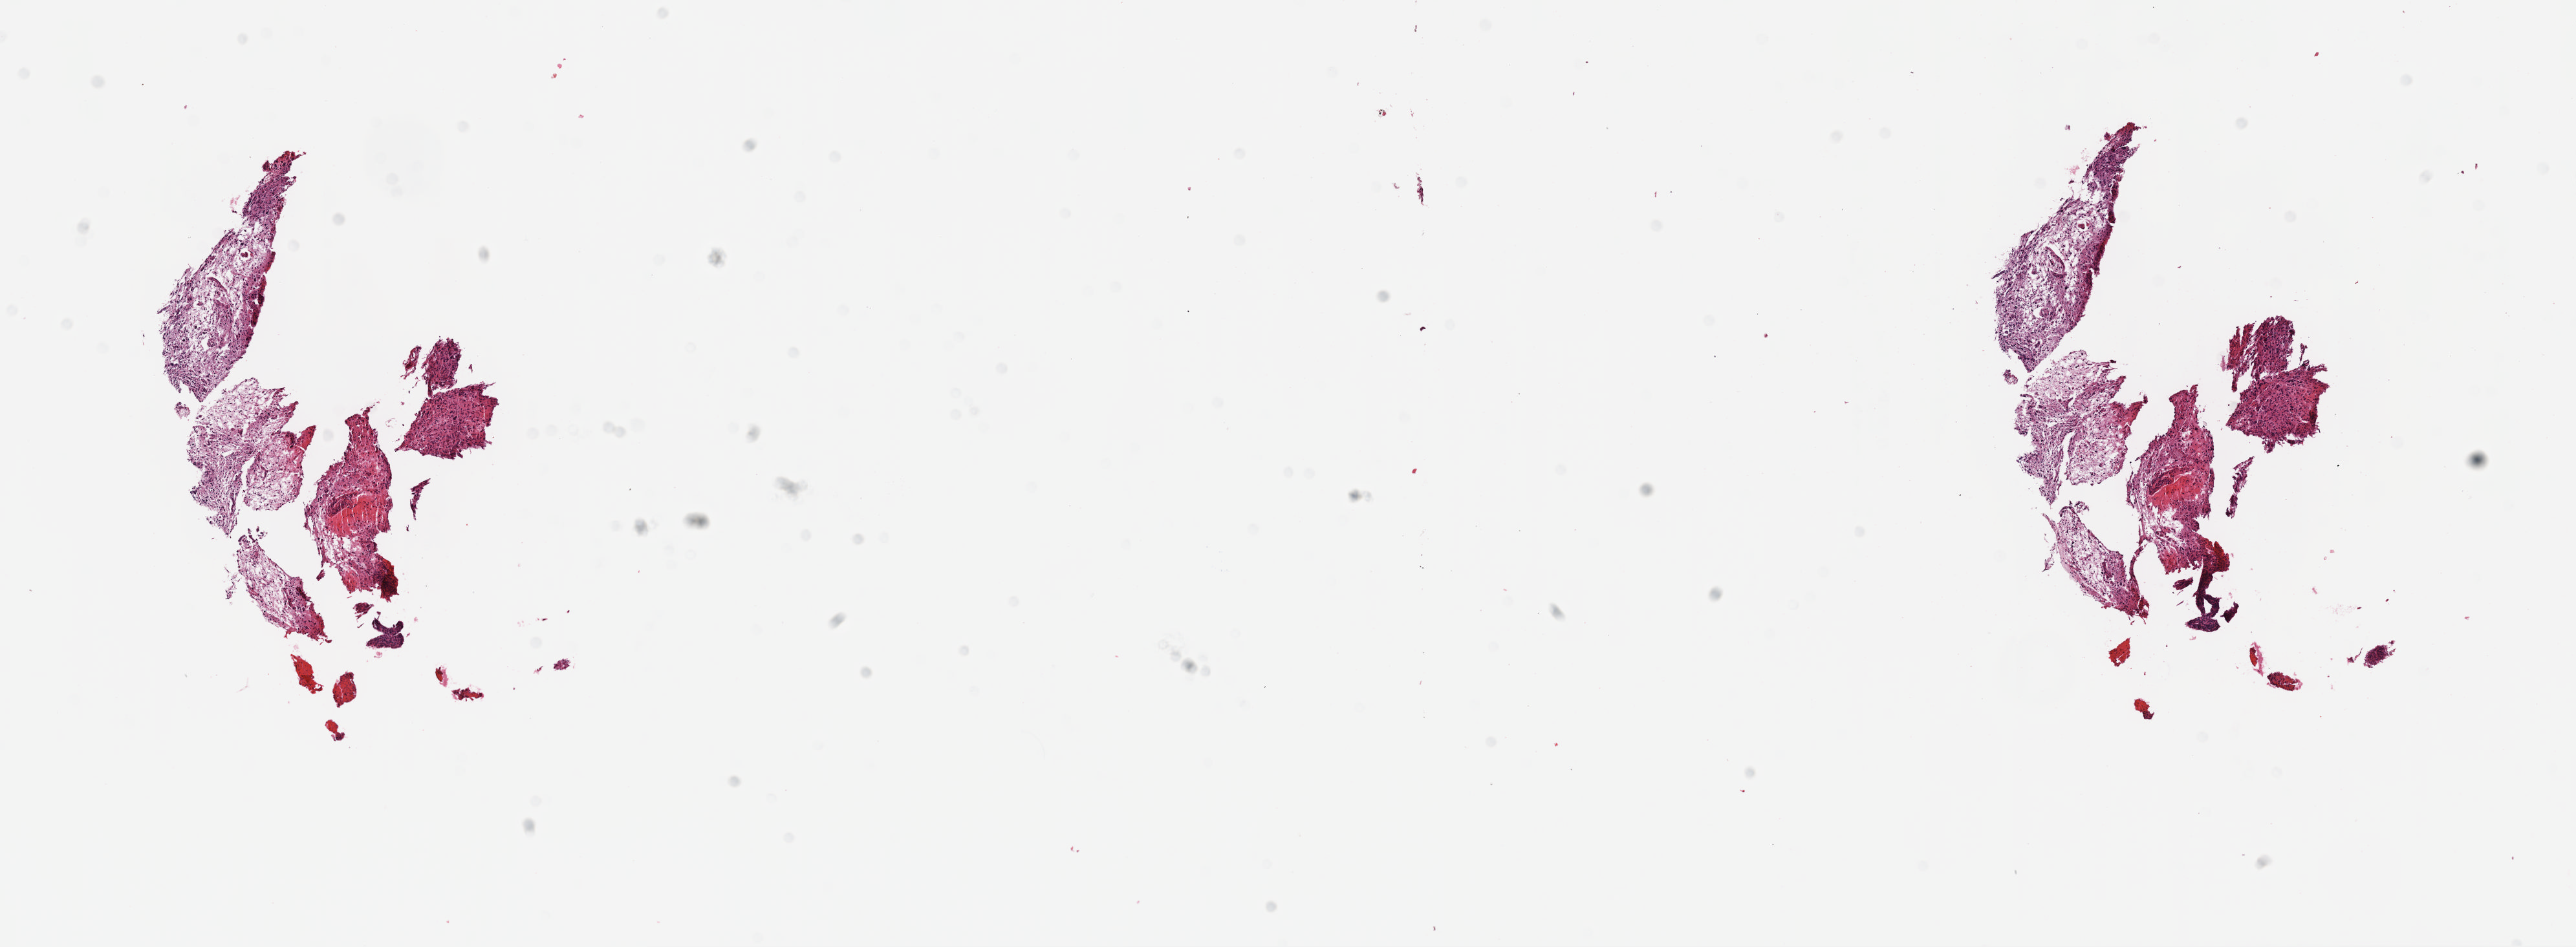
Whole-slide histology image, H&E-stained — shown as a low-resolution overview of the whole scanned area (about 16.1 x 5.9 mm), formalin-fixed paraffin-embedded (FFPE) diagnostic section, brain, primary tumour sample. Patient: female, age at initial diagnosis 24 years. Histologic grade: G3 (poorly differentiated).
Laterality: left. Histologic diagnosis: Astrocytoma, anaplastic (cerebrum).